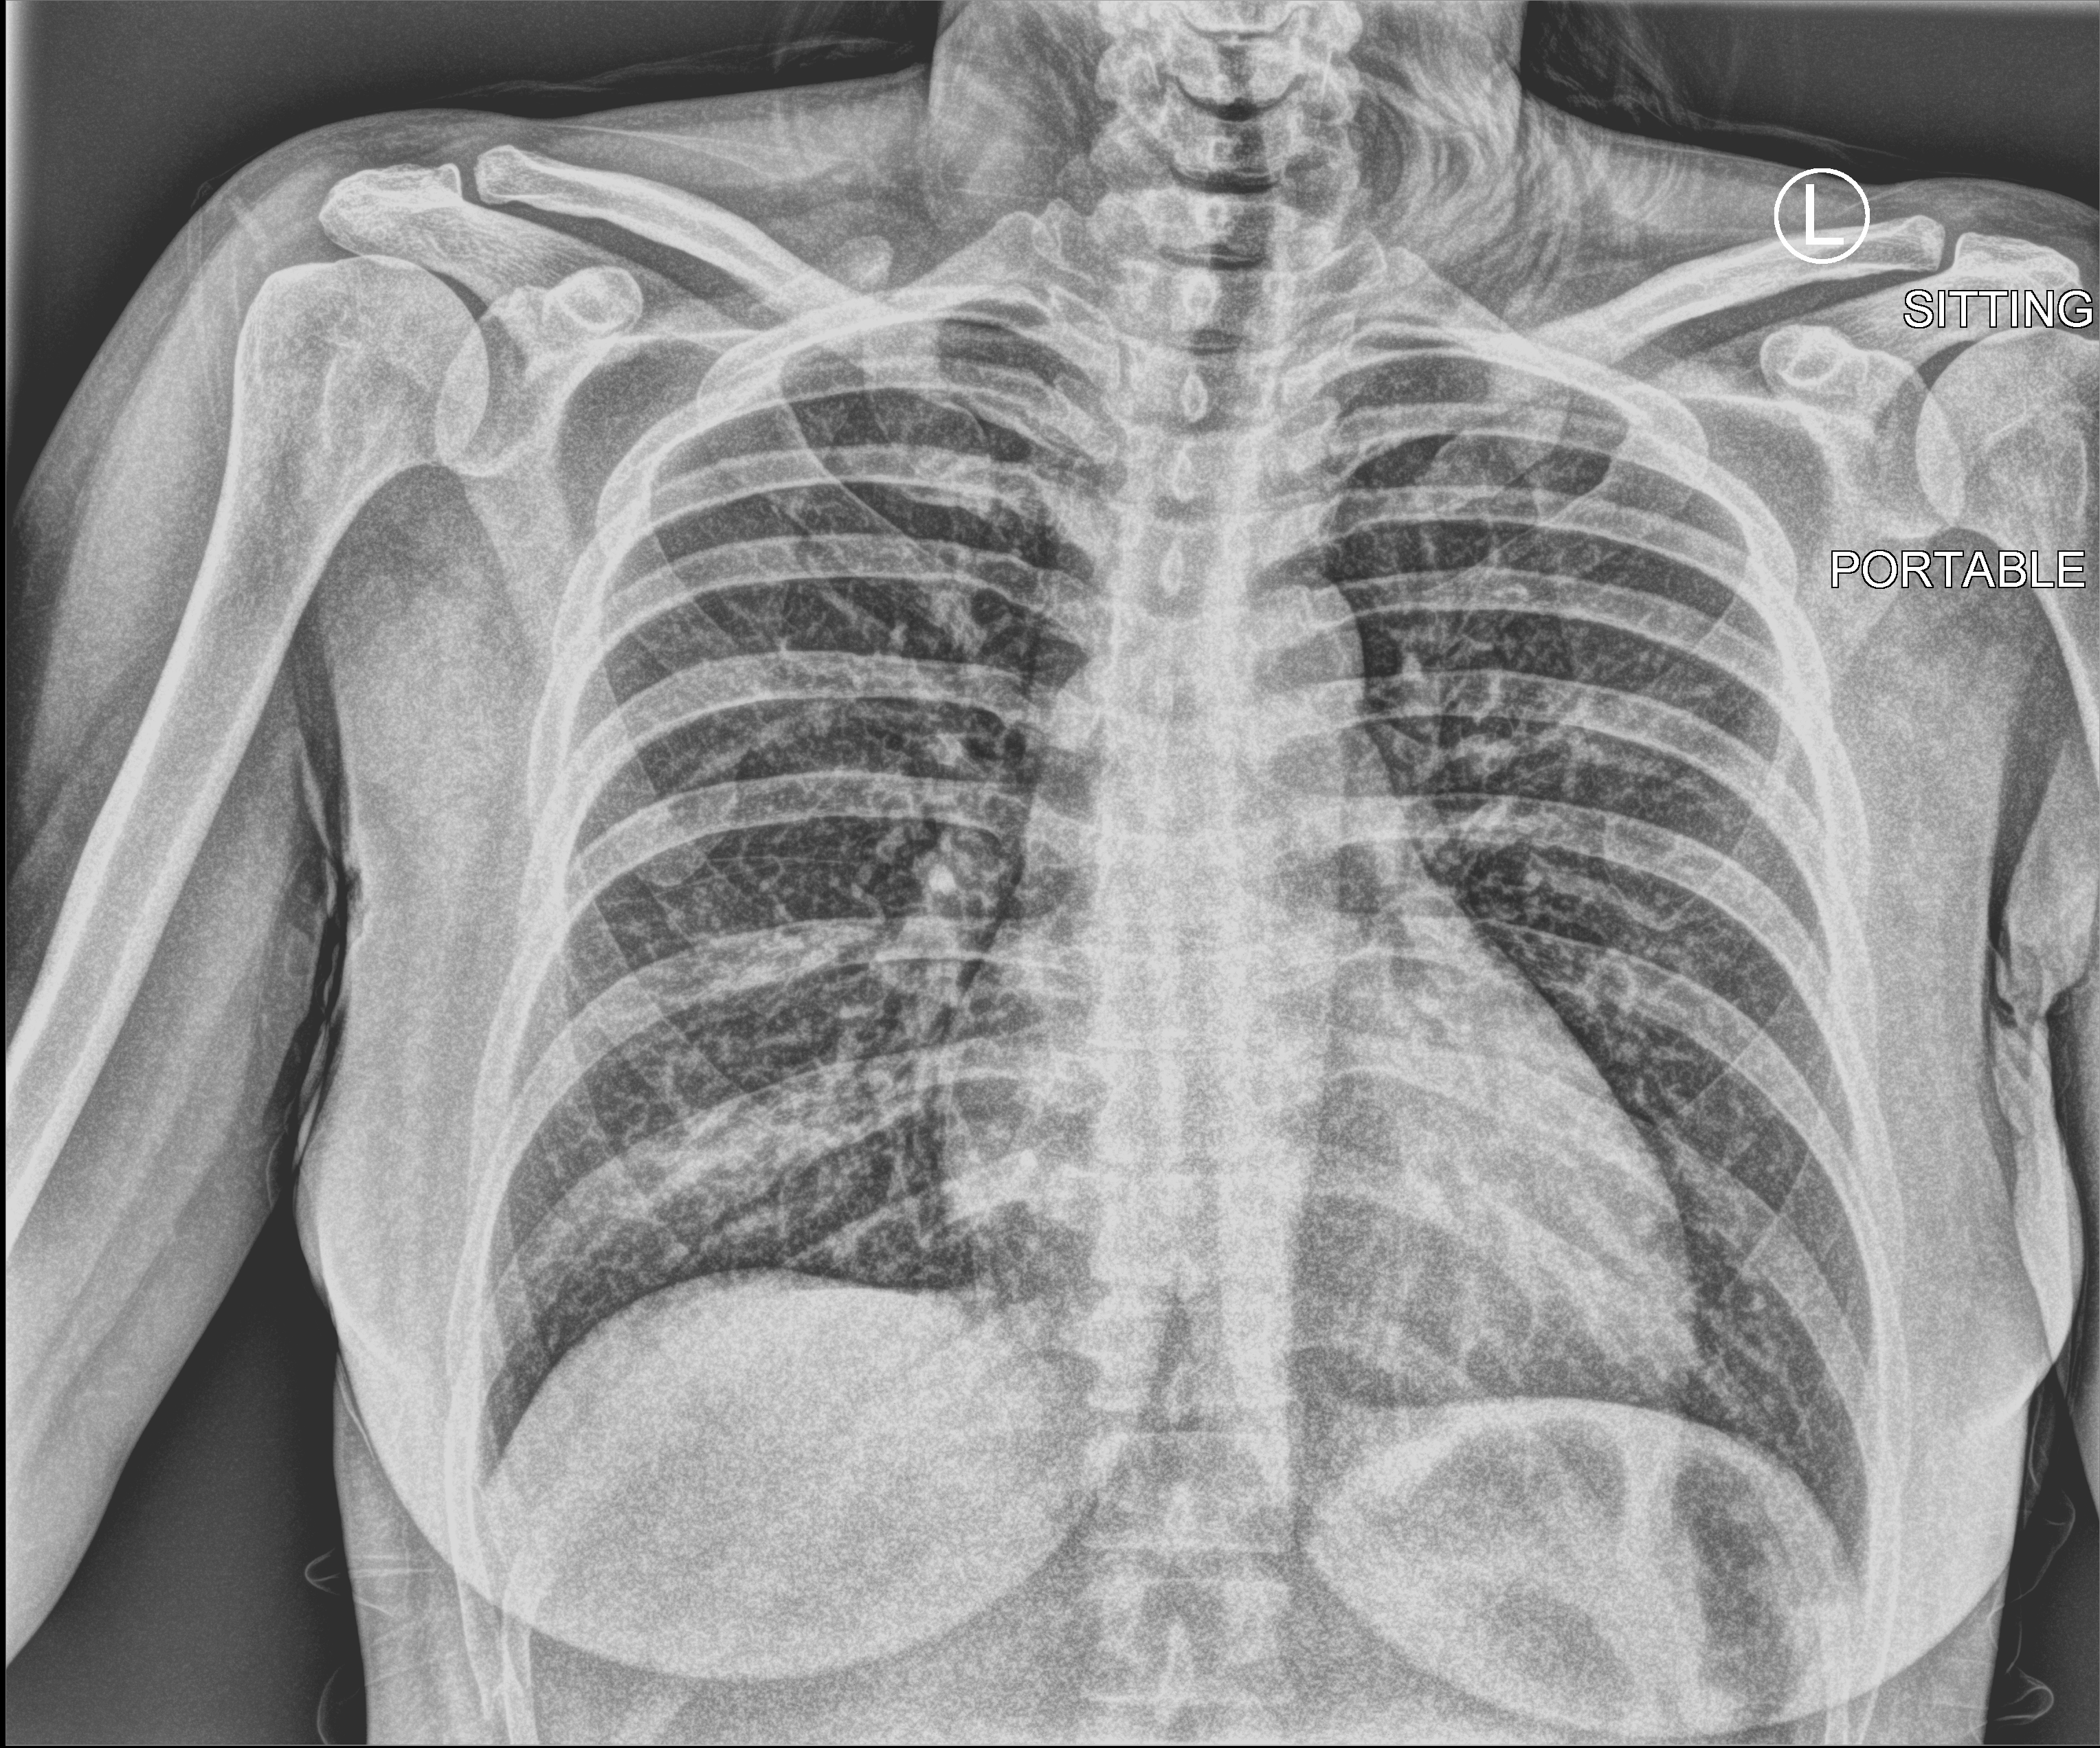
Portable chest radiograph. Female patient hospitalised with COVID-19, age 18–59 years.
Hospital-stay facts (about this admission, not read from this image; timing relative to this image not recorded): mechanically ventilated during this hospital stay: no.